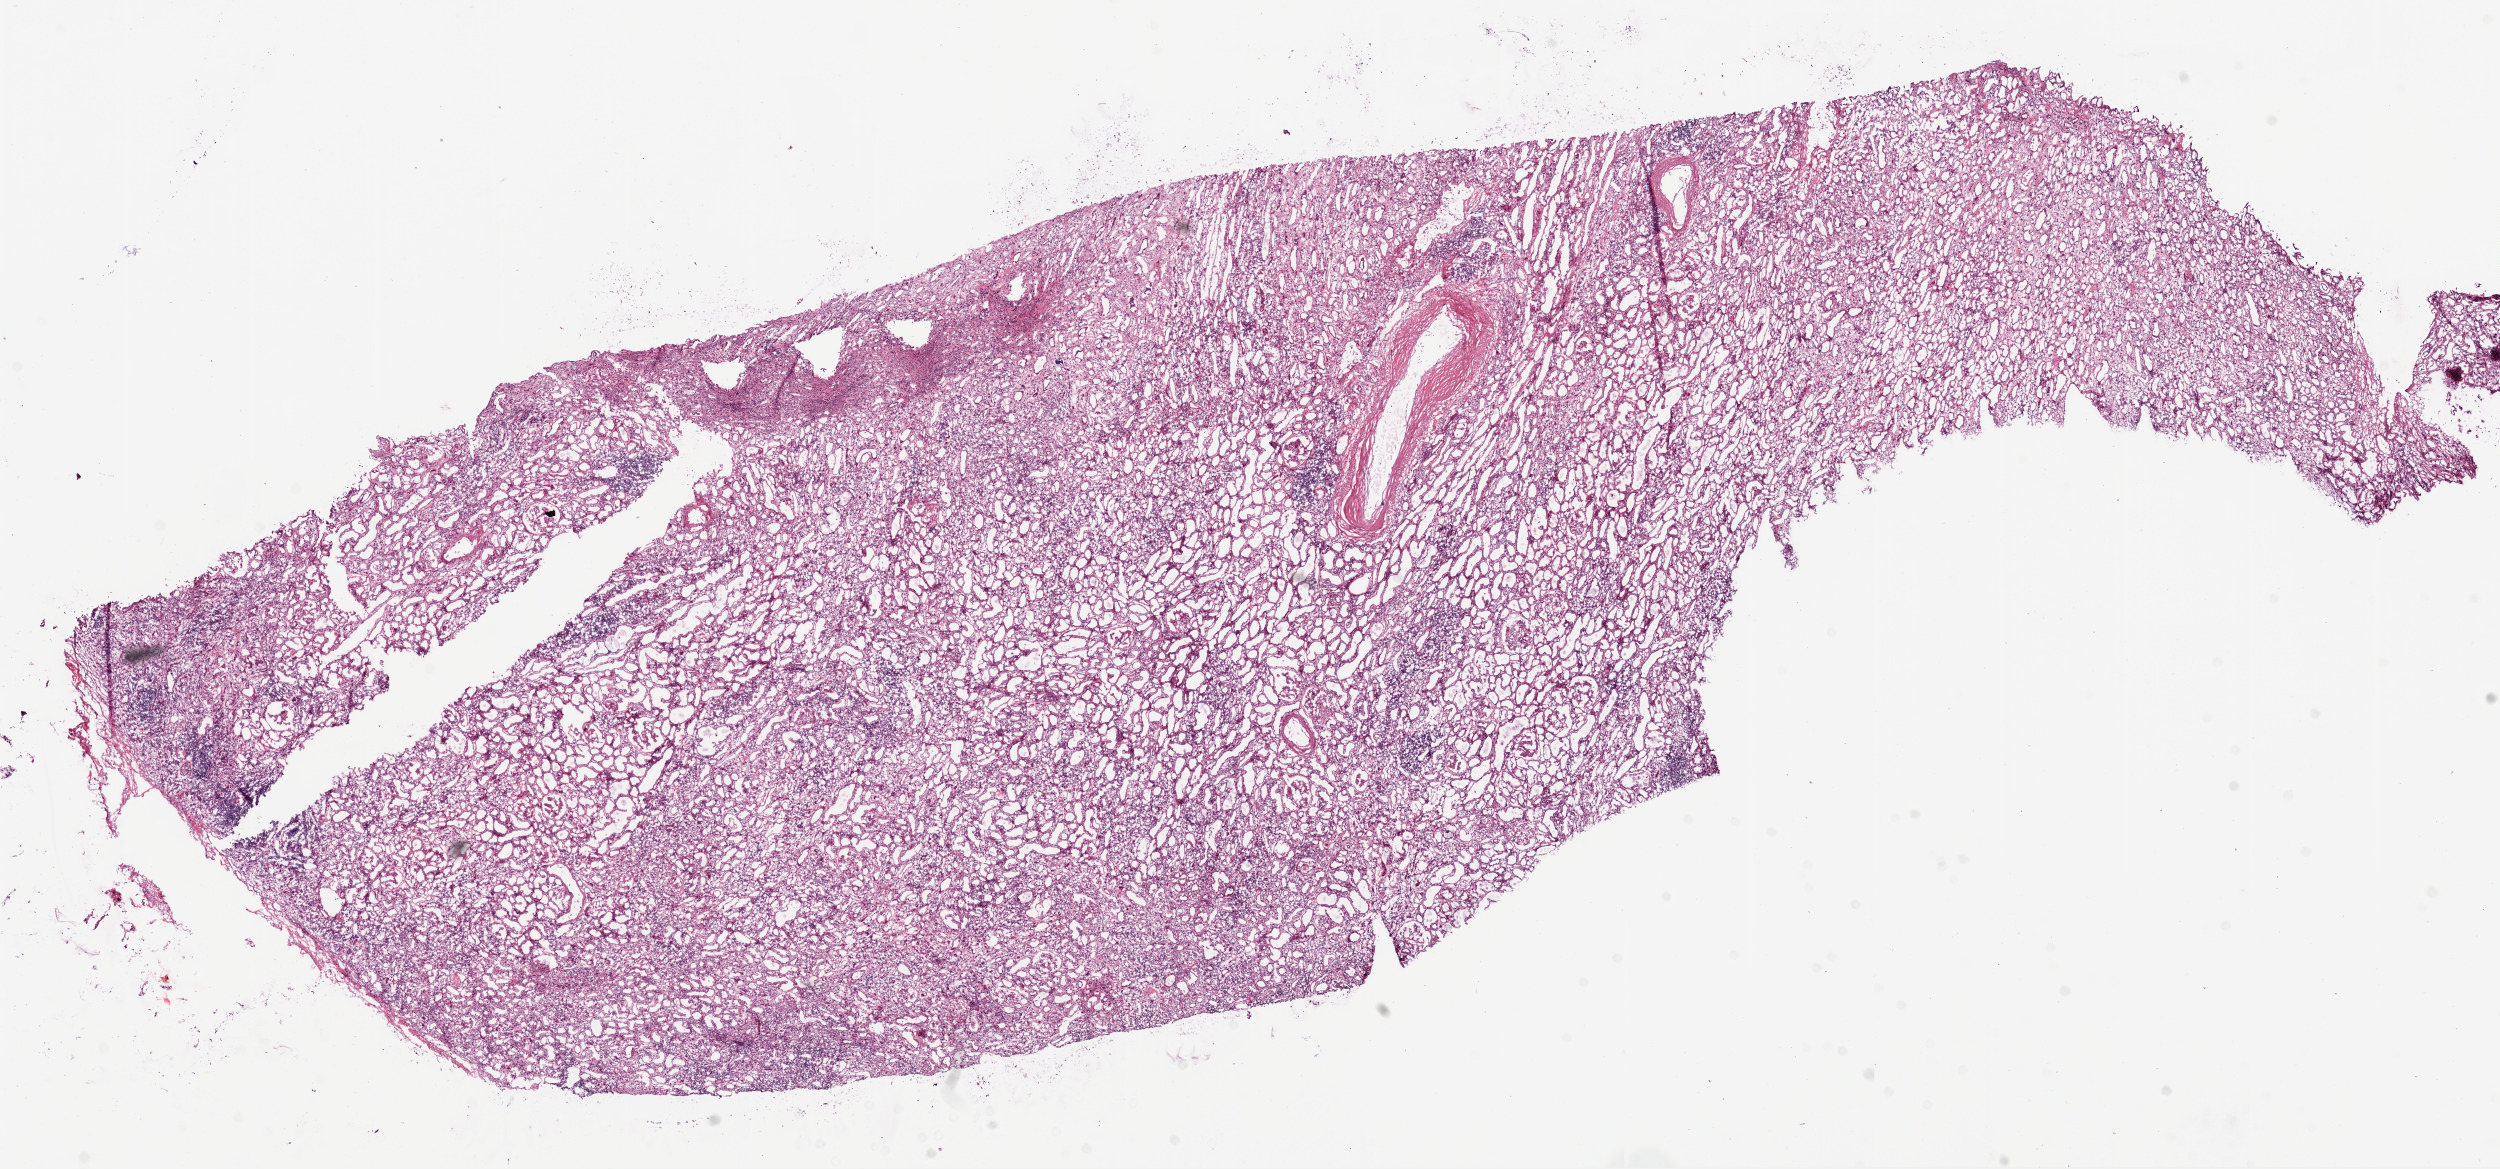
H&E-stained whole-slide image, a low-resolution overview of the entire scanned area, about 20.1 x 9.4 mm (slide scanned at 20x), frozen section from the bottom of the tissue portion, sample: solid tissue normal (non-tumour tissue), kidney. Patient: female, age at initial diagnosis 68 years.
• this section: solid tissue normal (non-tumour) sample from the same patient
• patient diagnosis: Clear cell adenocarcinoma, NOS